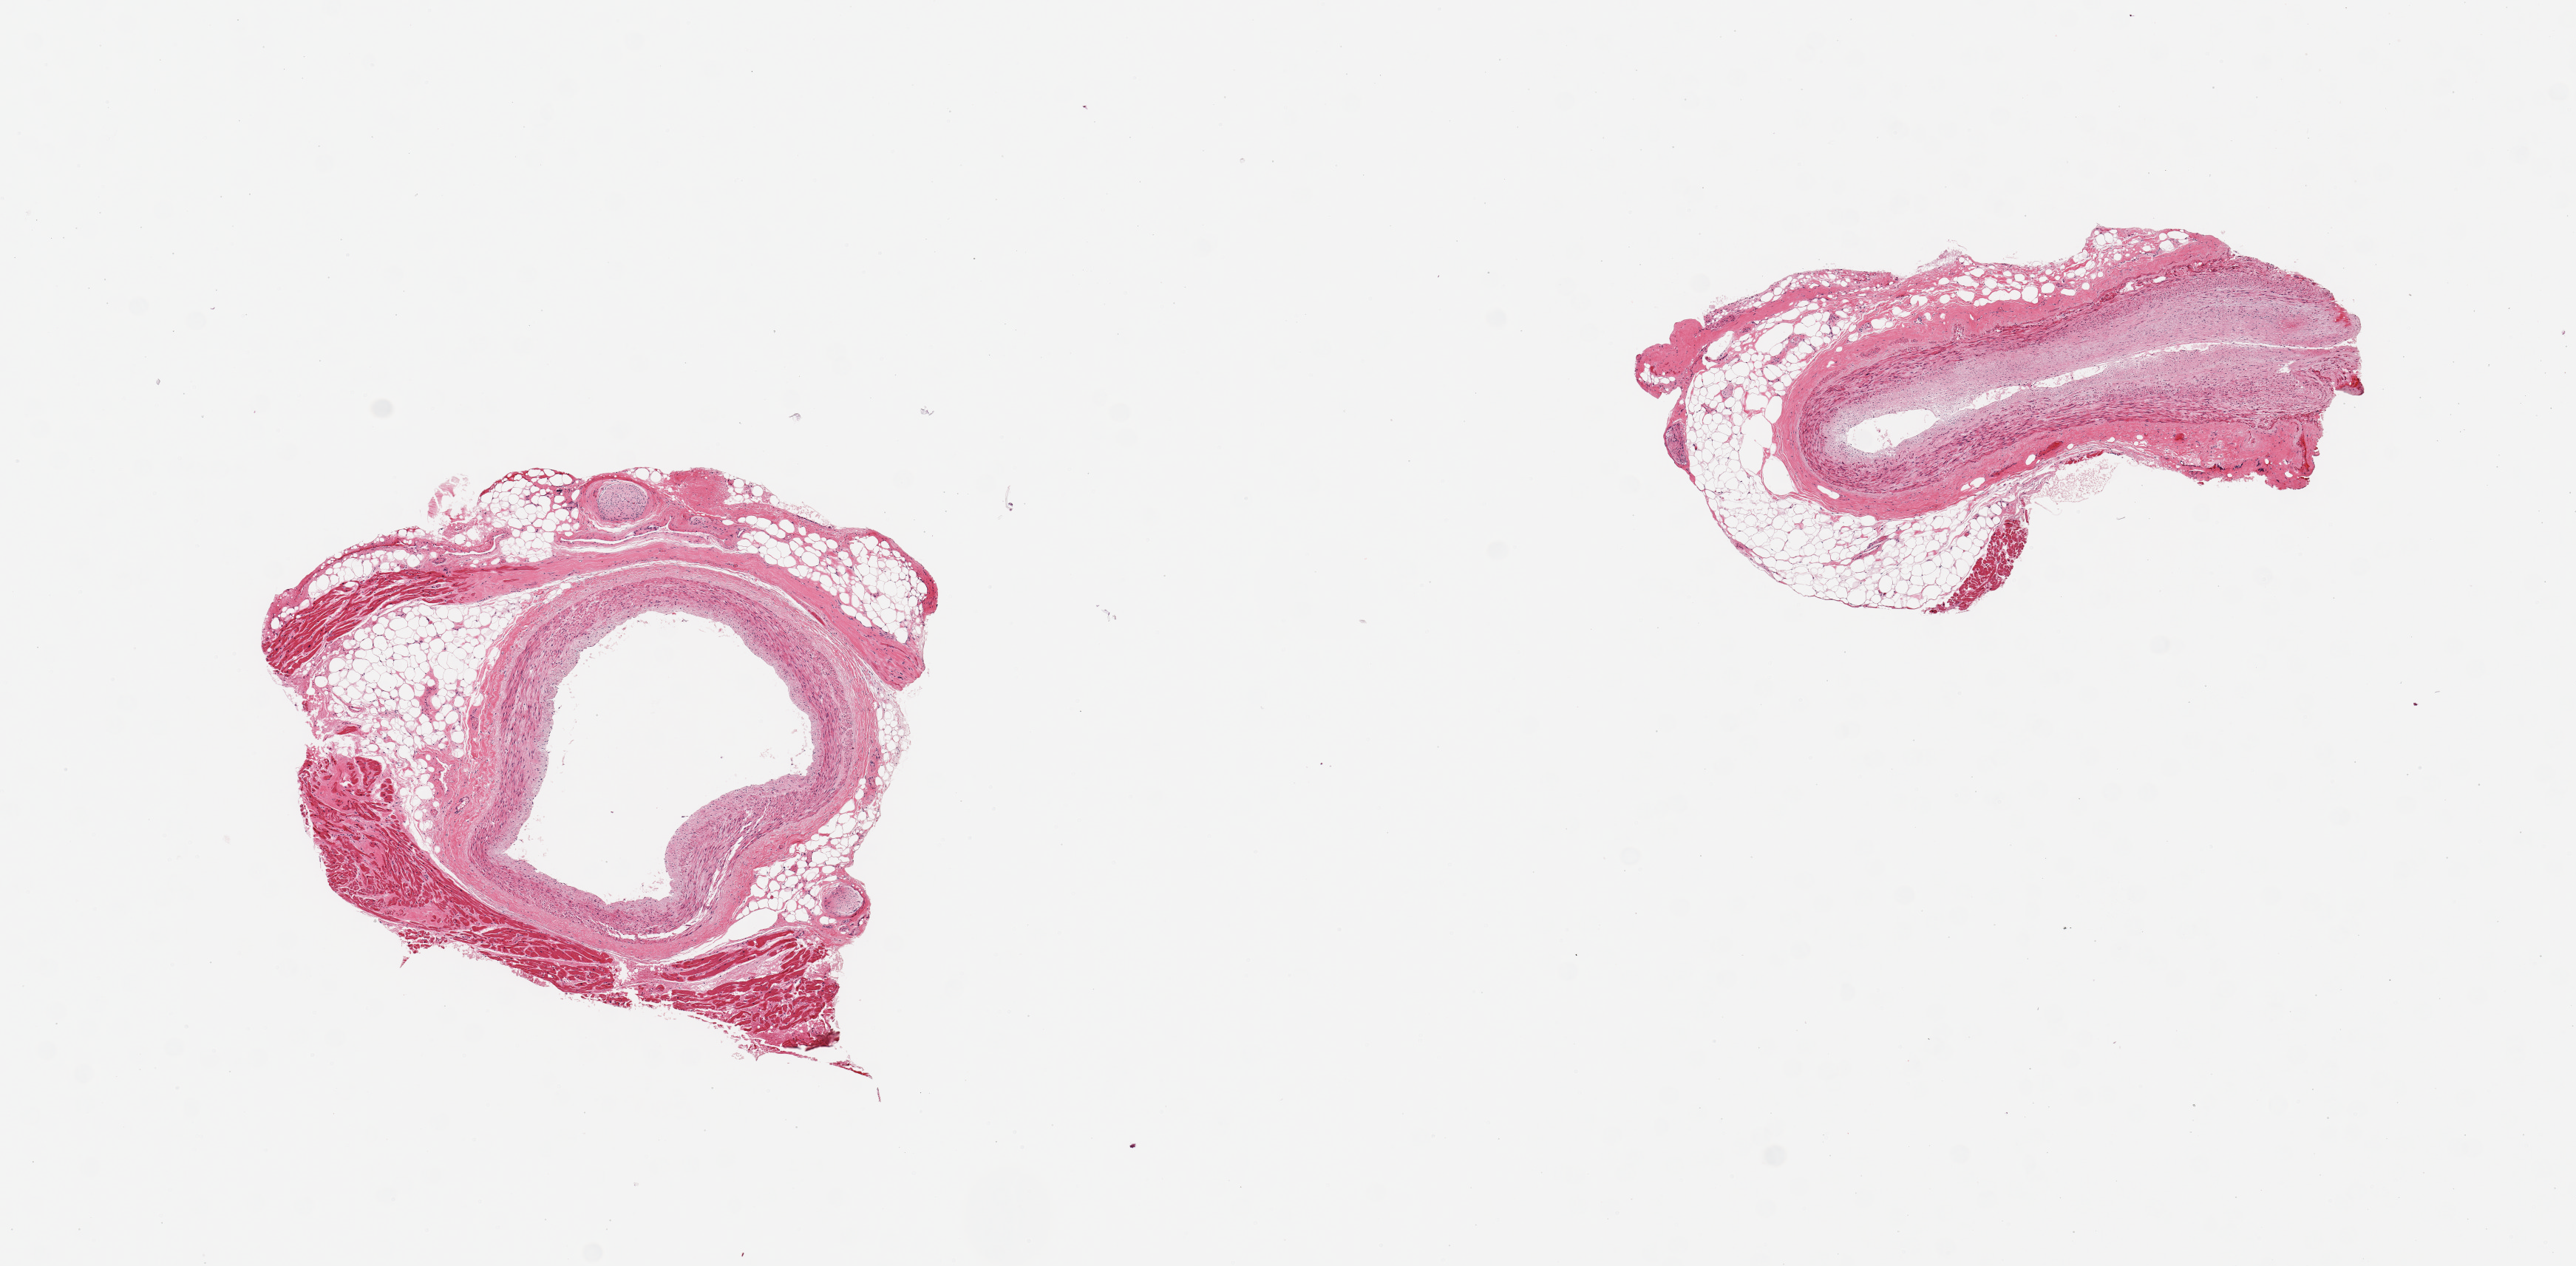
Whole-slide image, haematoxylin and eosin stain, low-resolution overview of the scanned area, about 13.8 x 6.8 mm; PAXgene-fixed, paraffin-embedded tissue; section of coronary artery (target tissue); donor tissue sample.
Pathologist's review note for this sample: 2 pieces, both with rim of attached fat, nerve, and cardiac muscle comprising 30-70% of the specimens.